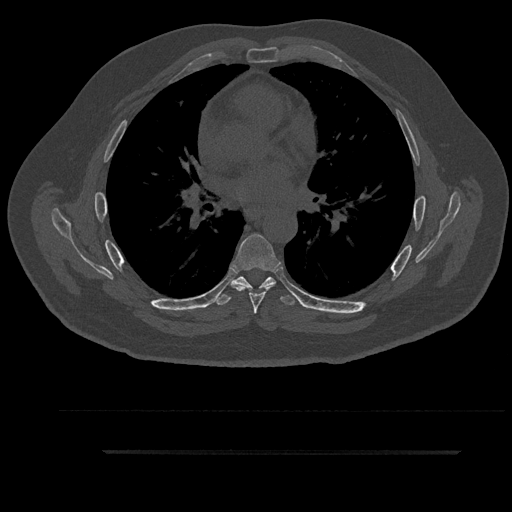
CT including the spine, one axial slice. Slice 560 of 797 in the series (ordered by position). Reconstruction kernel Br40s/3. 120 kVp. Bone window (W 1800 / L 400 HU). 512 × 512 image matrix, field of view 432 × 432 mm. Male patient, age 63 years. Case-level facts recorded for this patient, not image findings: primary cancer: renal; vertebrae with lytic lesions (as recorded): T8.
Annotated regions visible in this slice (semi-automatic segmentation, software-assisted and operator-edited):
- T5 vertebra: box from (x=240, y=276) to (x=271, y=291) px
- T6 vertebra: (x=231, y=234)–(x=281, y=314)
- T7 vertebra: (x=216, y=277)–(x=298, y=305)